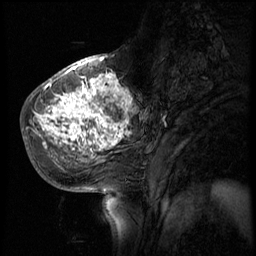
Breast MRI (dynamic contrast-enhanced), one sagittal slice; slice 23 of 56 in the series (ordered by position); 4 images stored at this slice position (order not interpretable as contrast timing); 1.5 T; TE 4.2 ms, TR 8.9 ms; 2.5 mm slice thickness; 256 × 256 image matrix, field of view 220 × 220 mm. Female patient, age 51 years. Case-level facts recorded for this patient, not image findings: setting: breast cancer imaged before/during neoadjuvant chemotherapy; receptor status: triple-negative.
Annotated regions visible in this slice (semi-automatically segmented with operator editing):
- analysis volume of interest (the breast-tissue region the enhancement analysis was run in; not a lesion): bounding box (x1, y1, x2, y2) in pixels: (30, 70, 150, 173)
- tumour enhancement mask (voxels above the 140 % enhancement threshold inside the analysis volume of interest): (34, 70, 136, 153)